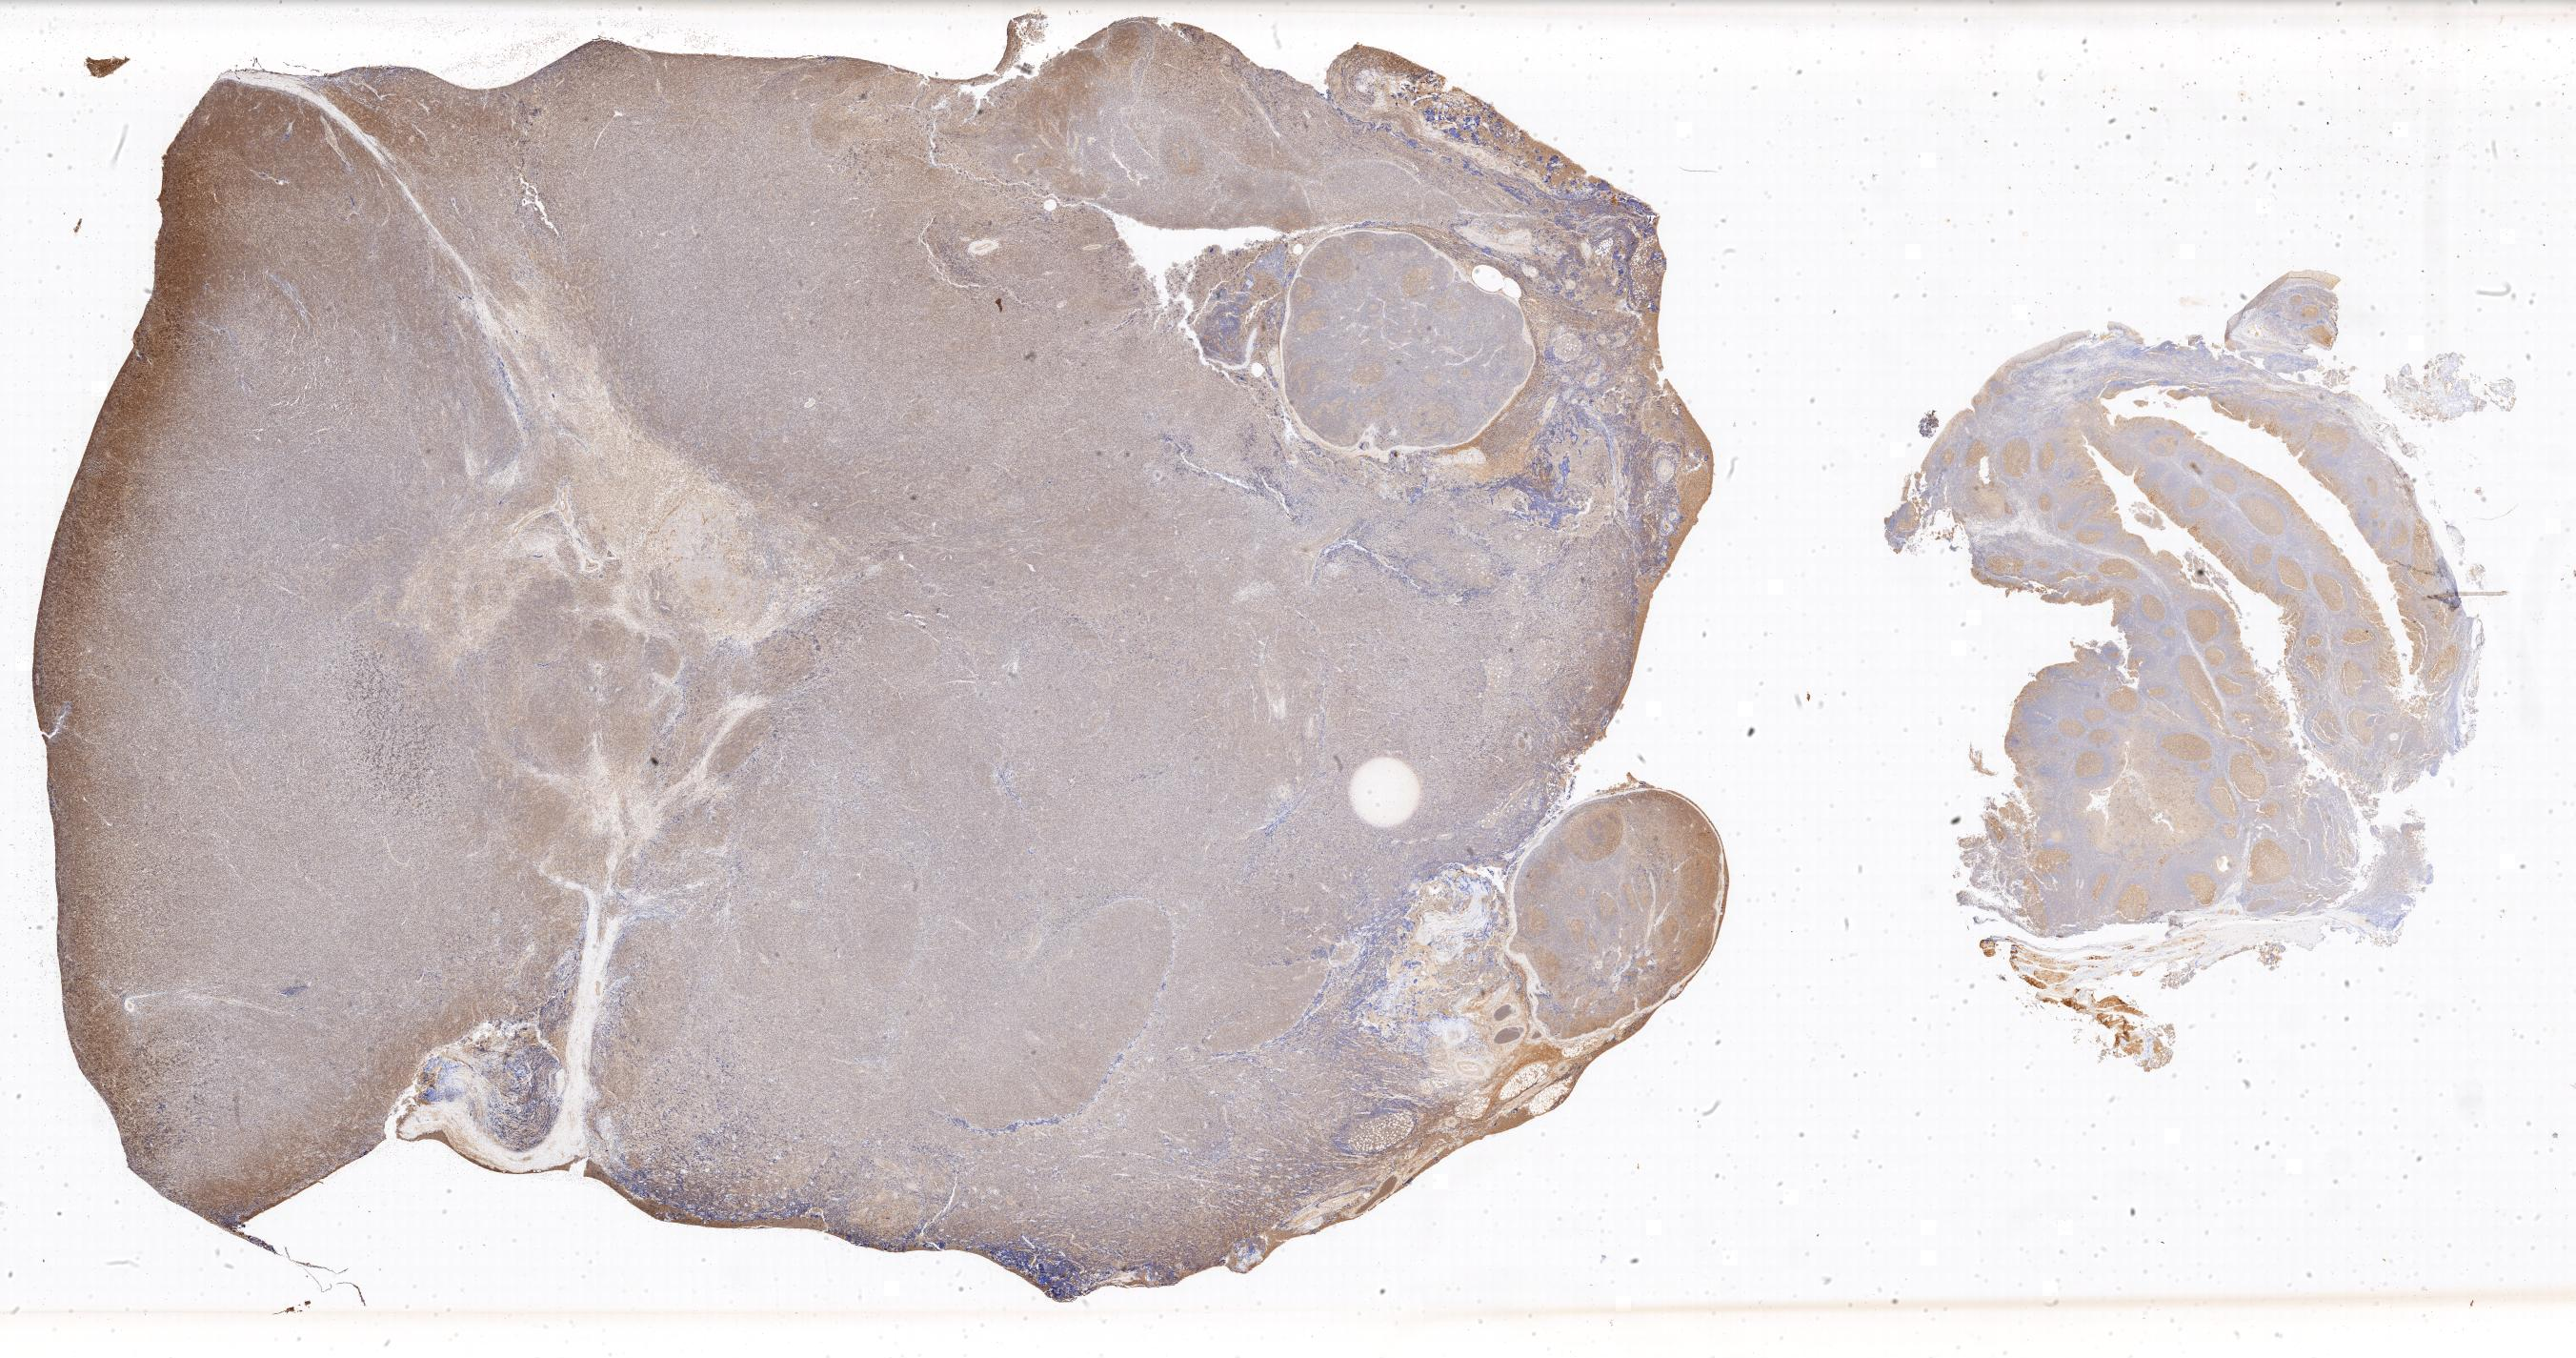
Whole-slide image, immunohistochemical stain for BCL6 — whole scanned area shown as a low-resolution overview, specimen: tumor tissue, site: lymph node of head and neck. Male patient; age at initial diagnosis 3 years.
- diagnosis: Burkitt lymphoma, NOS